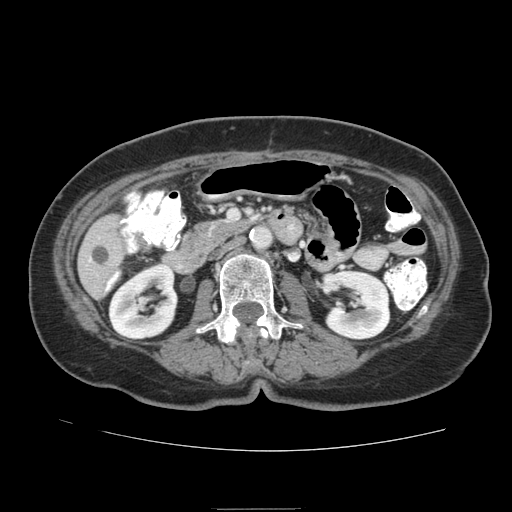
Contrast-enhanced abdominal CT (liver protocol), one axial slice; slice 25 of 95 in the series (ordered by position); reconstruction kernel STANDARD; soft-tissue window (W 400 / L 40 HU); 2.5 mm slice thickness; 512 × 512 image matrix. From the clinical record (not read from this slice): diagnosis: hepatocellular carcinoma (patient treated with transarterial chemoembolisation; whether this scan precedes or follows treatment is not stated here); TNM stage (as recorded): Stage-IVA; Child-Pugh class: B; tumour differentiation: moderately differentiated; tumour nodularity: uninodular.
Annotated regions visible in this slice (semi-automatic segmentation, software-assisted and operator-edited):
- liver parenchyma outside the tumour (the mass and vessels are separate outlines, so this box may not span the whole liver): bounding box (x1, y1, x2, y2) in pixels: (78, 214, 126, 300)
- liver vessels: (89, 220, 124, 291)